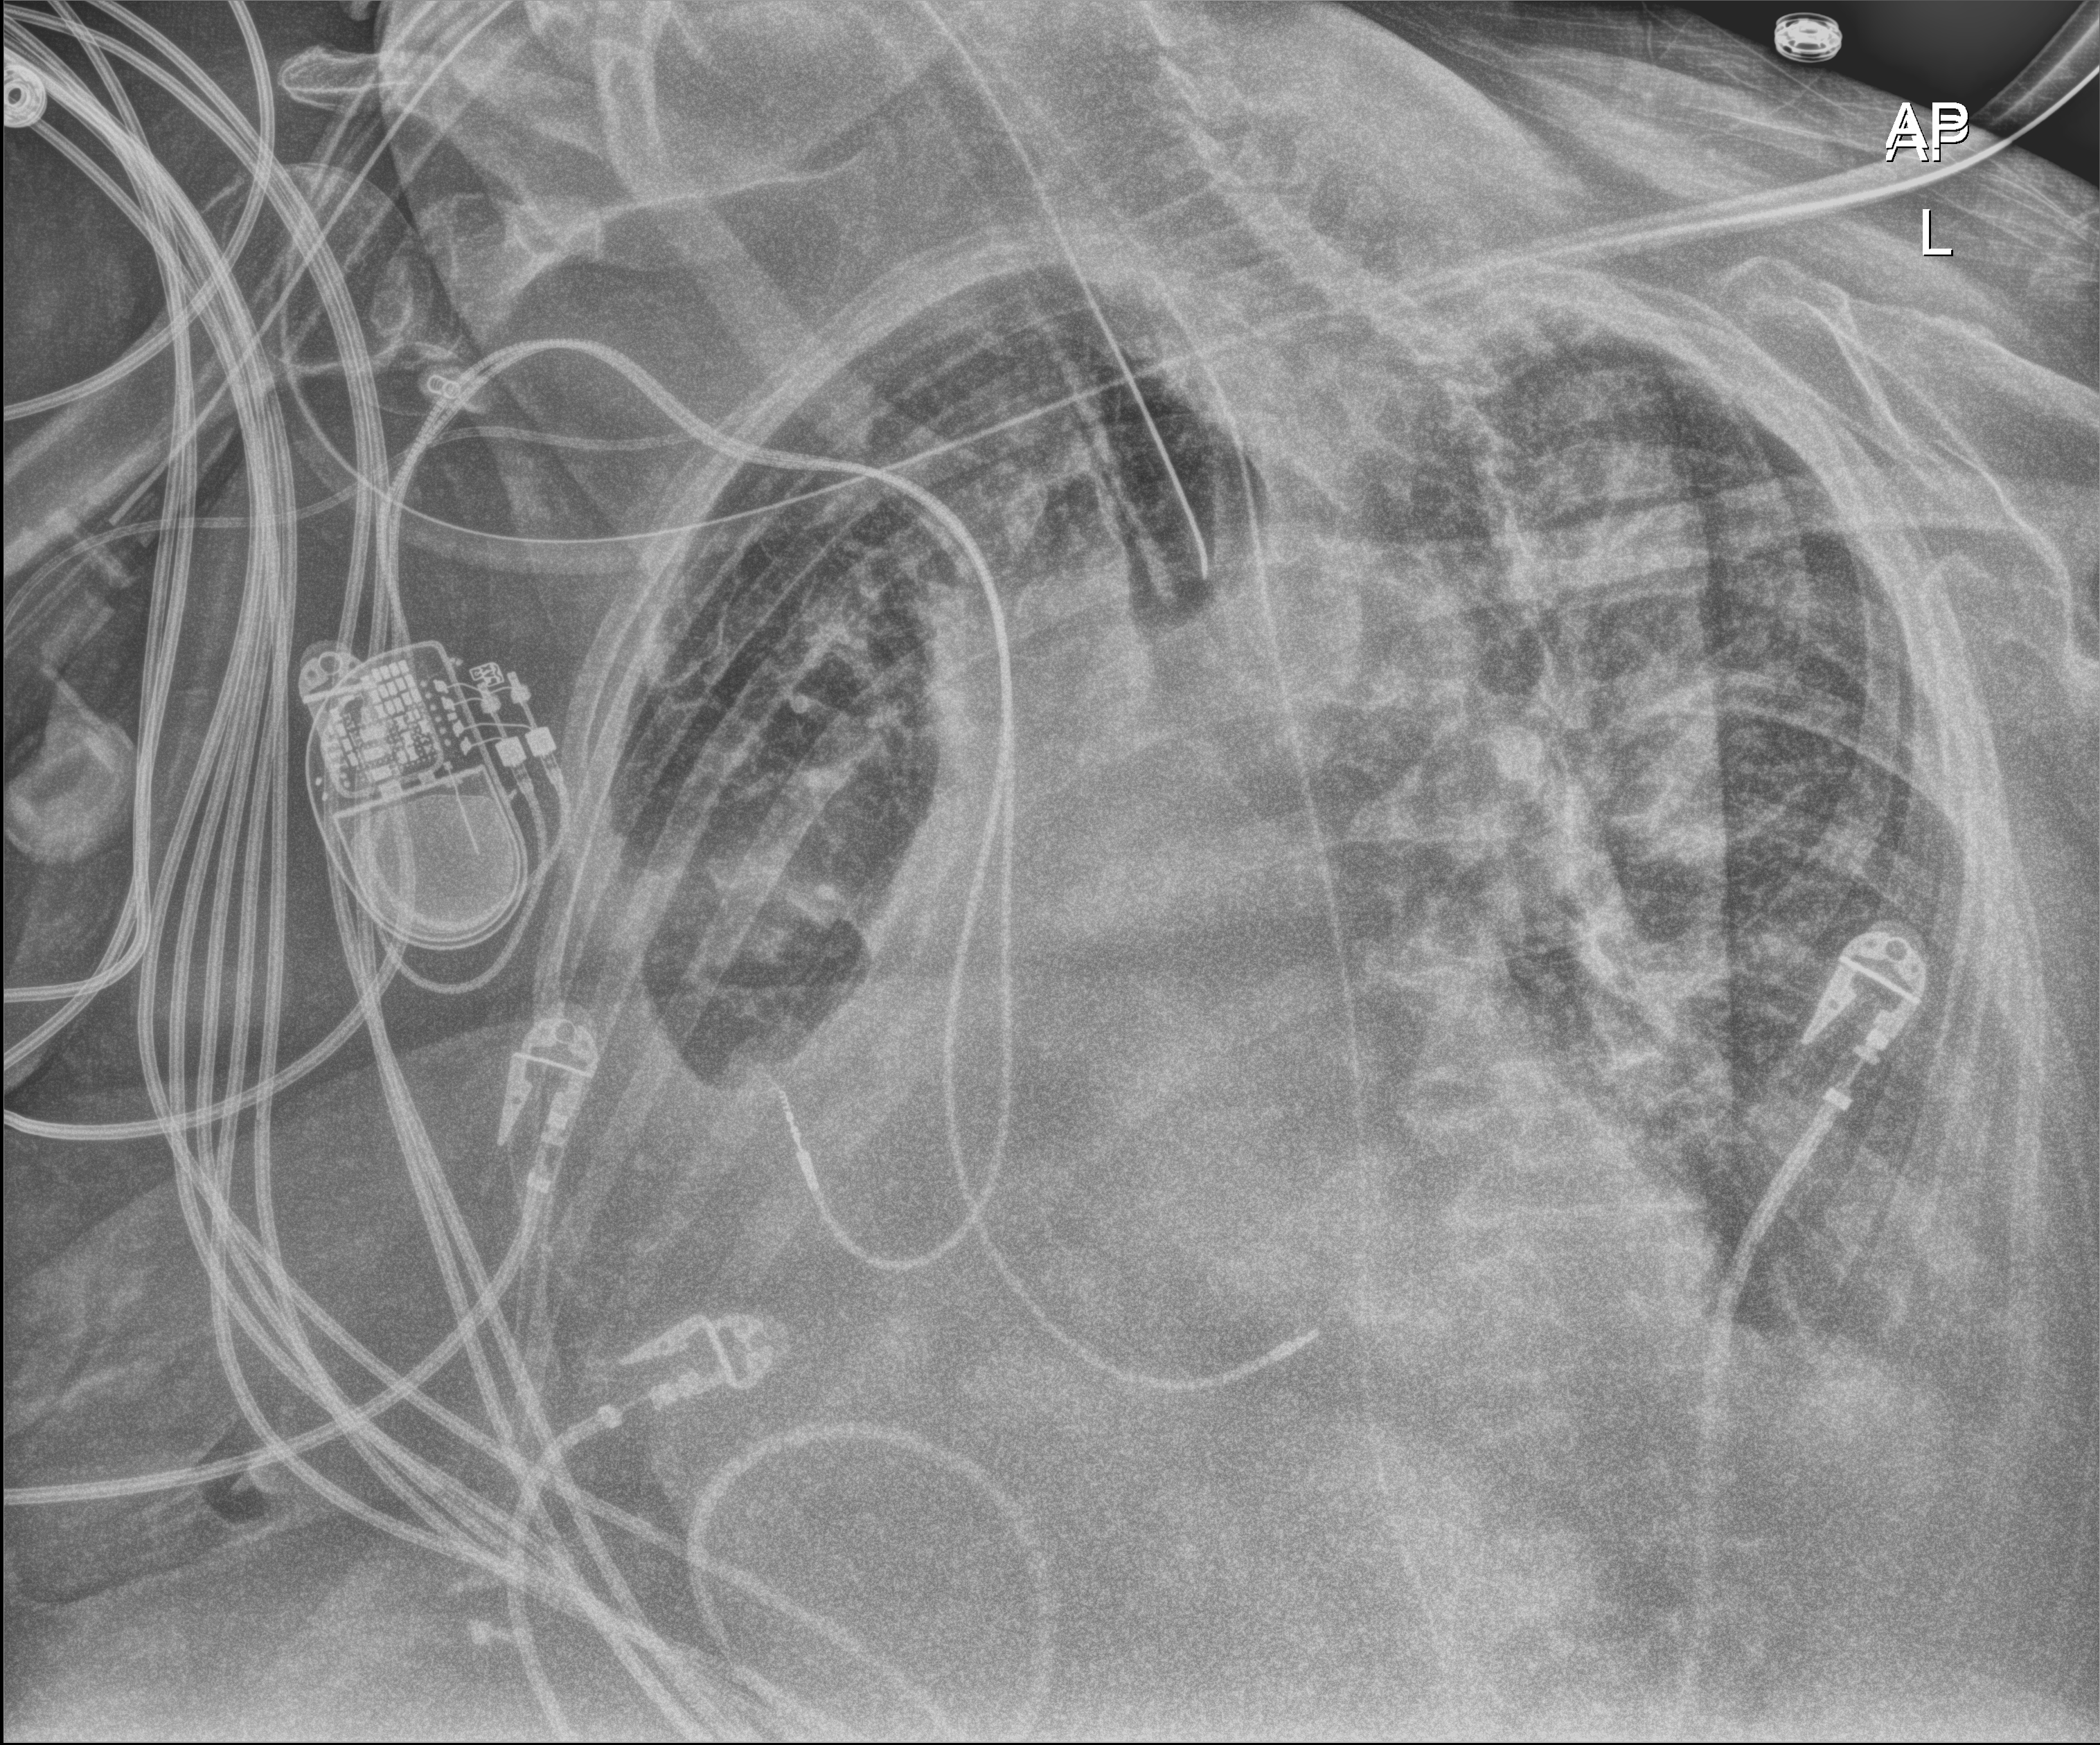
Chest X-ray (portable), anteroposterior (AP) projection. Patient hospitalised with COVID-19; female, aged 75–90 years.
From the hospital-stay record, not from the radiograph (when in the stay this image was taken is not recorded): other chronic lung disease (admission record): yes; admitted to intensive care during this hospital stay: yes.